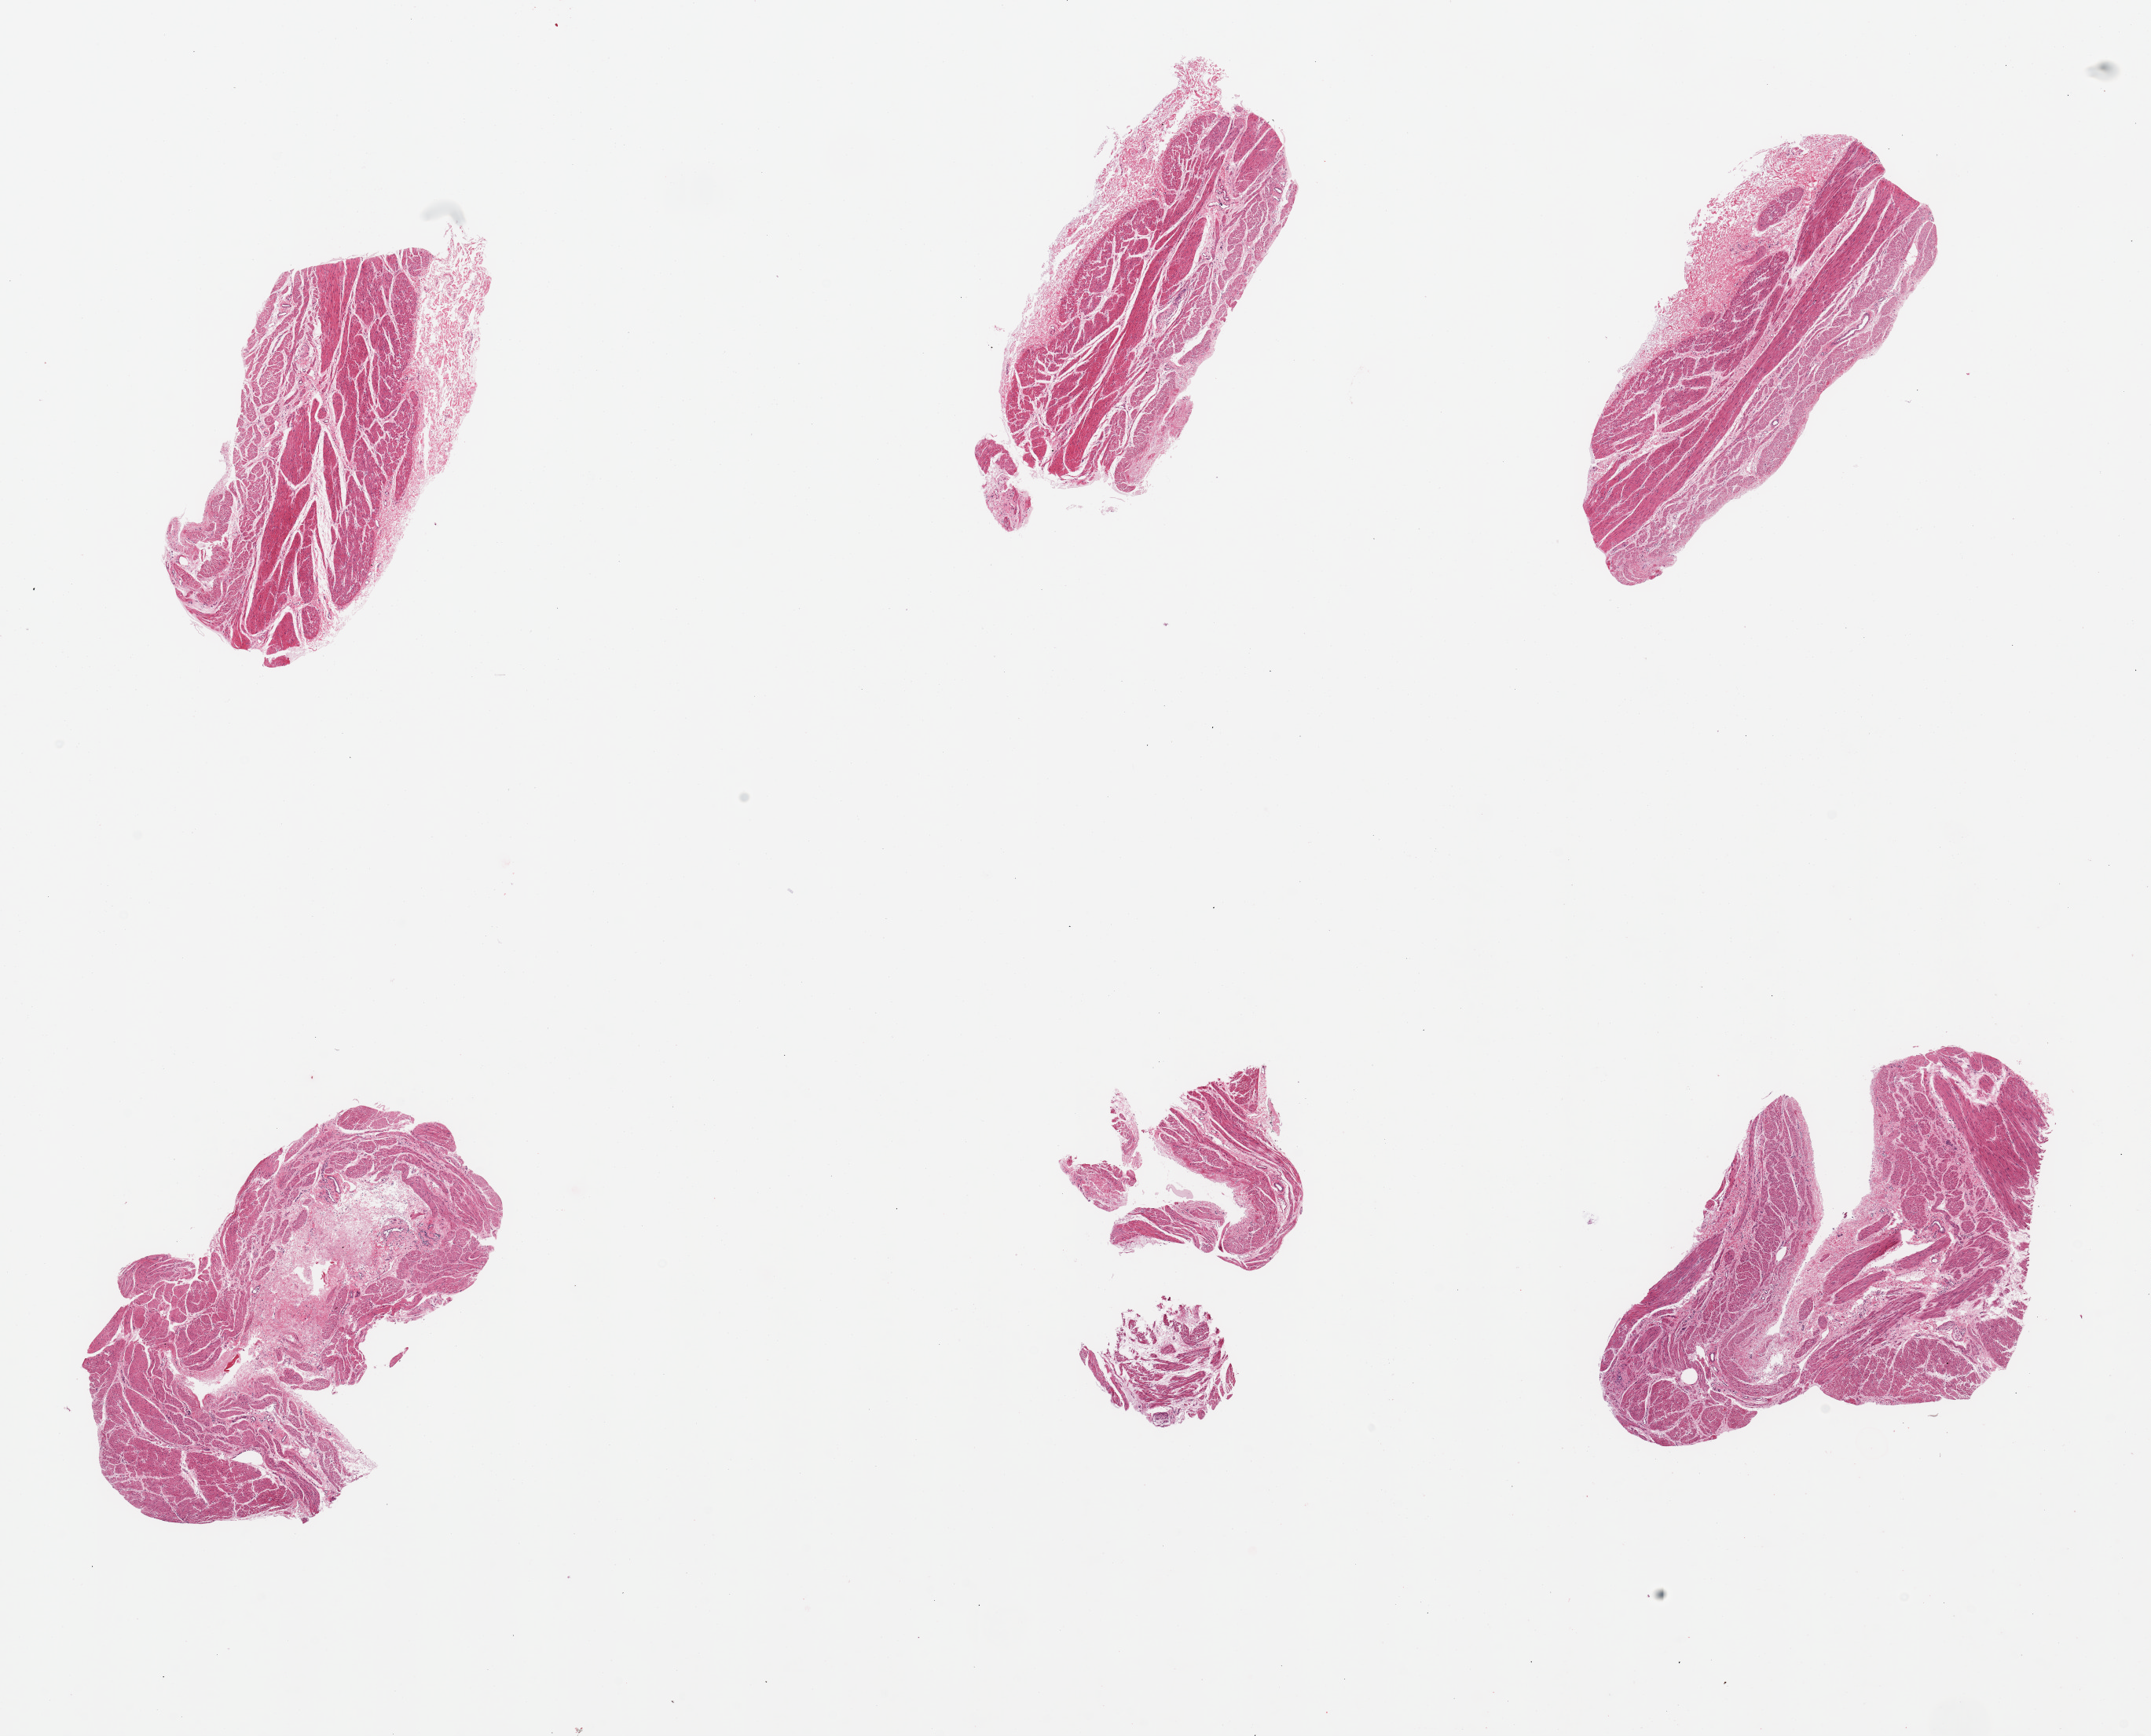
Whole-slide image, hematoxylin and eosin (H&E) stain — whole scanned area (about 21.7 x 17.5 mm) shown as a low-resolution overview. PAXgene-fixed, paraffin-embedded tissue. Section of stomach (target tissue). Donor tissue sample. Donor sex: male.
Review note (as recorded): 6 pieces; muscularis only, no mucosa.